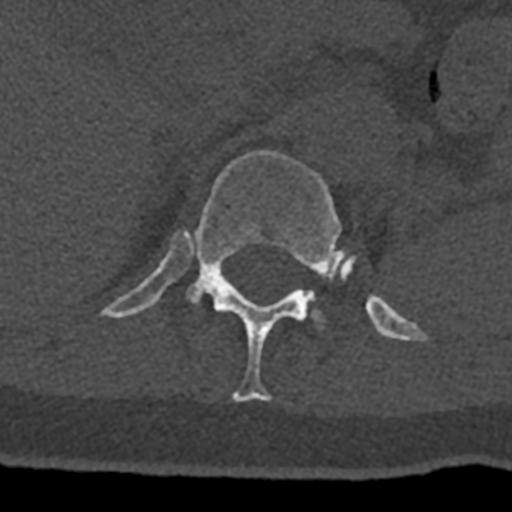
CT including the spine, one axial slice. Position 490 of 797 along the scan axis. Reconstruction kernel Br40s/3. 120 kVp. Bone window (W 1800 / L 400 HU). 512 × 512 image matrix, field of view 160 × 160 mm. Patient: male, 74 years. Case-level facts recorded for this patient, not image findings: primary cancer: renal; vertebrae with lytic lesions (as recorded): T10, L1, L2, L3, L4, L5.
Annotated regions visible in this slice (semi-automatically segmented with operator editing):
- L1 vertebra: box from (x=308, y=298) to (x=325, y=326) px
- T12 vertebra: (x=103, y=150)–(x=428, y=402)